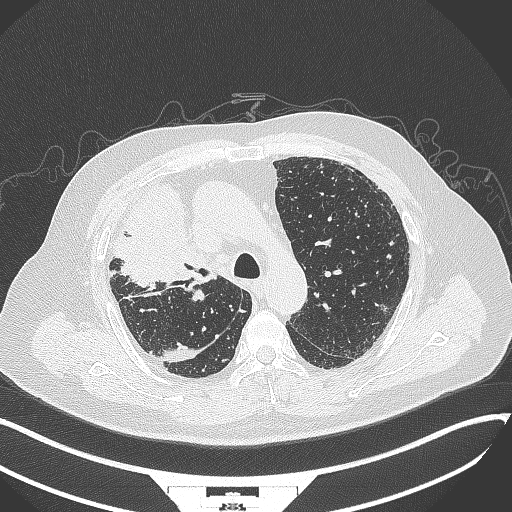
Chest CT, one axial slice. Position 250 of 384 along the scan axis. Lung window (W 1500 / L -600 HU). 512 × 512 image matrix, field of view 400 × 400 mm. Male patient, age 69 years. Case-level facts recorded for this patient, not image findings: clinical TNM (as recorded): T4 N3 M1.
Structures marked on this image (bounding box drawn by a radiologist):
- lung tumour (recorded histology: adenocarcinoma): box from (x=110, y=181) to (x=208, y=286) px